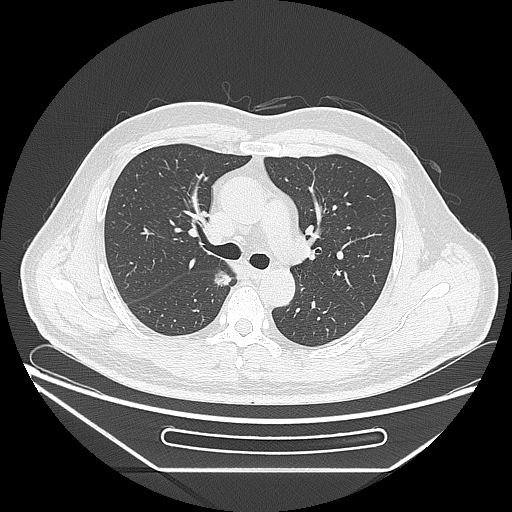
Chest CT, one axial slice. Slice 163 of 271 in the series (ordered by position). Reconstruction kernel LUNG. Lung window (W 1500 / L -600 HU). 1.25 mm slice thickness. 512 × 512 image matrix, field of view 414 × 414 mm. Male patient, age 49 years. Case-level facts recorded for this patient, not image findings: clinical TNM (as recorded): T1b N0 M0; histopathological grade: G2.
Outlined on this slice (rectangle marked by the reading radiologist):
- lung tumour (recorded histology: adenocarcinoma): bounding box (x1, y1, x2, y2) in pixels: (213, 269, 237, 295)